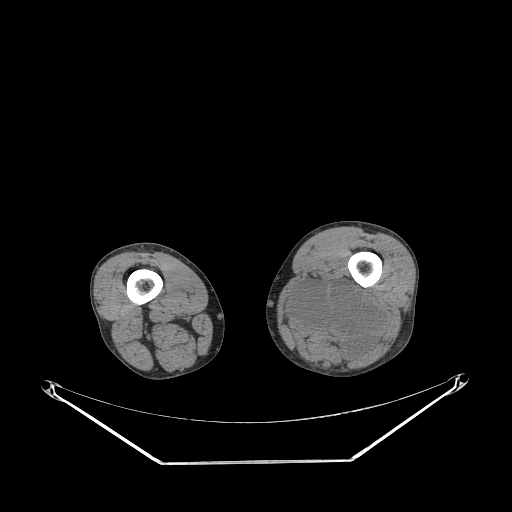
CT of an extremity soft-tissue mass (from a PET/CT study), one axial slice. Slice 213 of 267 in the series (ordered by position). Reconstruction kernel STANDARD. 140 kVp. Soft-tissue window (W 400 / L 40 HU). 3.75 mm slice thickness. 512 × 512 image matrix. Male patient. Case-level facts recorded for this patient, not image findings: histological type: undifferentiated pleomorphic liposarcoma; grade: high; site of the primary tumour: left thigh.
Outlined on this slice (expert contour drawn on MRI and transferred to this co-registered scan by the dataset authors):
- gross tumour volume including surrounding oedema: bounding box (x1, y1, x2, y2) in pixels: (288, 272, 382, 359)
- gross tumour volume (mass): (292, 283, 378, 353)